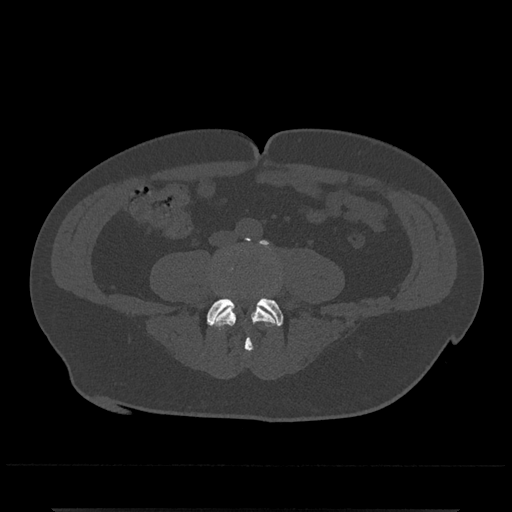
CT including the spine, one axial slice. Slice 122 of 797 in the series (ordered by position). Reconstruction kernel Br40s/3. 120 kVp. Bone window (W 1800 / L 400 HU). 0.5 mm slice thickness. 512 × 512 image matrix. Male patient, age 67 years. Case-level facts recorded for this patient, not image findings: primary cancer: prostate.
Annotated regions visible in this slice (semi-automatically segmented with operator editing):
- L4 vertebra: box from (x=210, y=240) to (x=282, y=352) px
- L5 vertebra: (x=207, y=297)–(x=283, y=326)